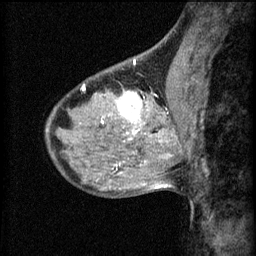
Breast MRI (dynamic contrast-enhanced), one sagittal slice; slice 26 of 60 in the series (ordered by position); 3 images stored at this slice position (order not interpretable as contrast timing); 1.5 T; TE 4.2 ms, TR 8.2 ms; 256 × 256 image matrix, field of view 180 × 180 mm. Patient: female, 40 years.
Structures marked on this image (semi-automatic segmentation, software-assisted and operator-edited):
- analysis volume of interest (the breast-tissue region the enhancement analysis was run in; not a lesion): bounding box [x1, y1, x2, y2] px = [108, 82, 175, 139]
- tumour enhancement mask (voxels above the 70 % enhancement threshold inside the analysis volume of interest): [118, 92, 165, 135]